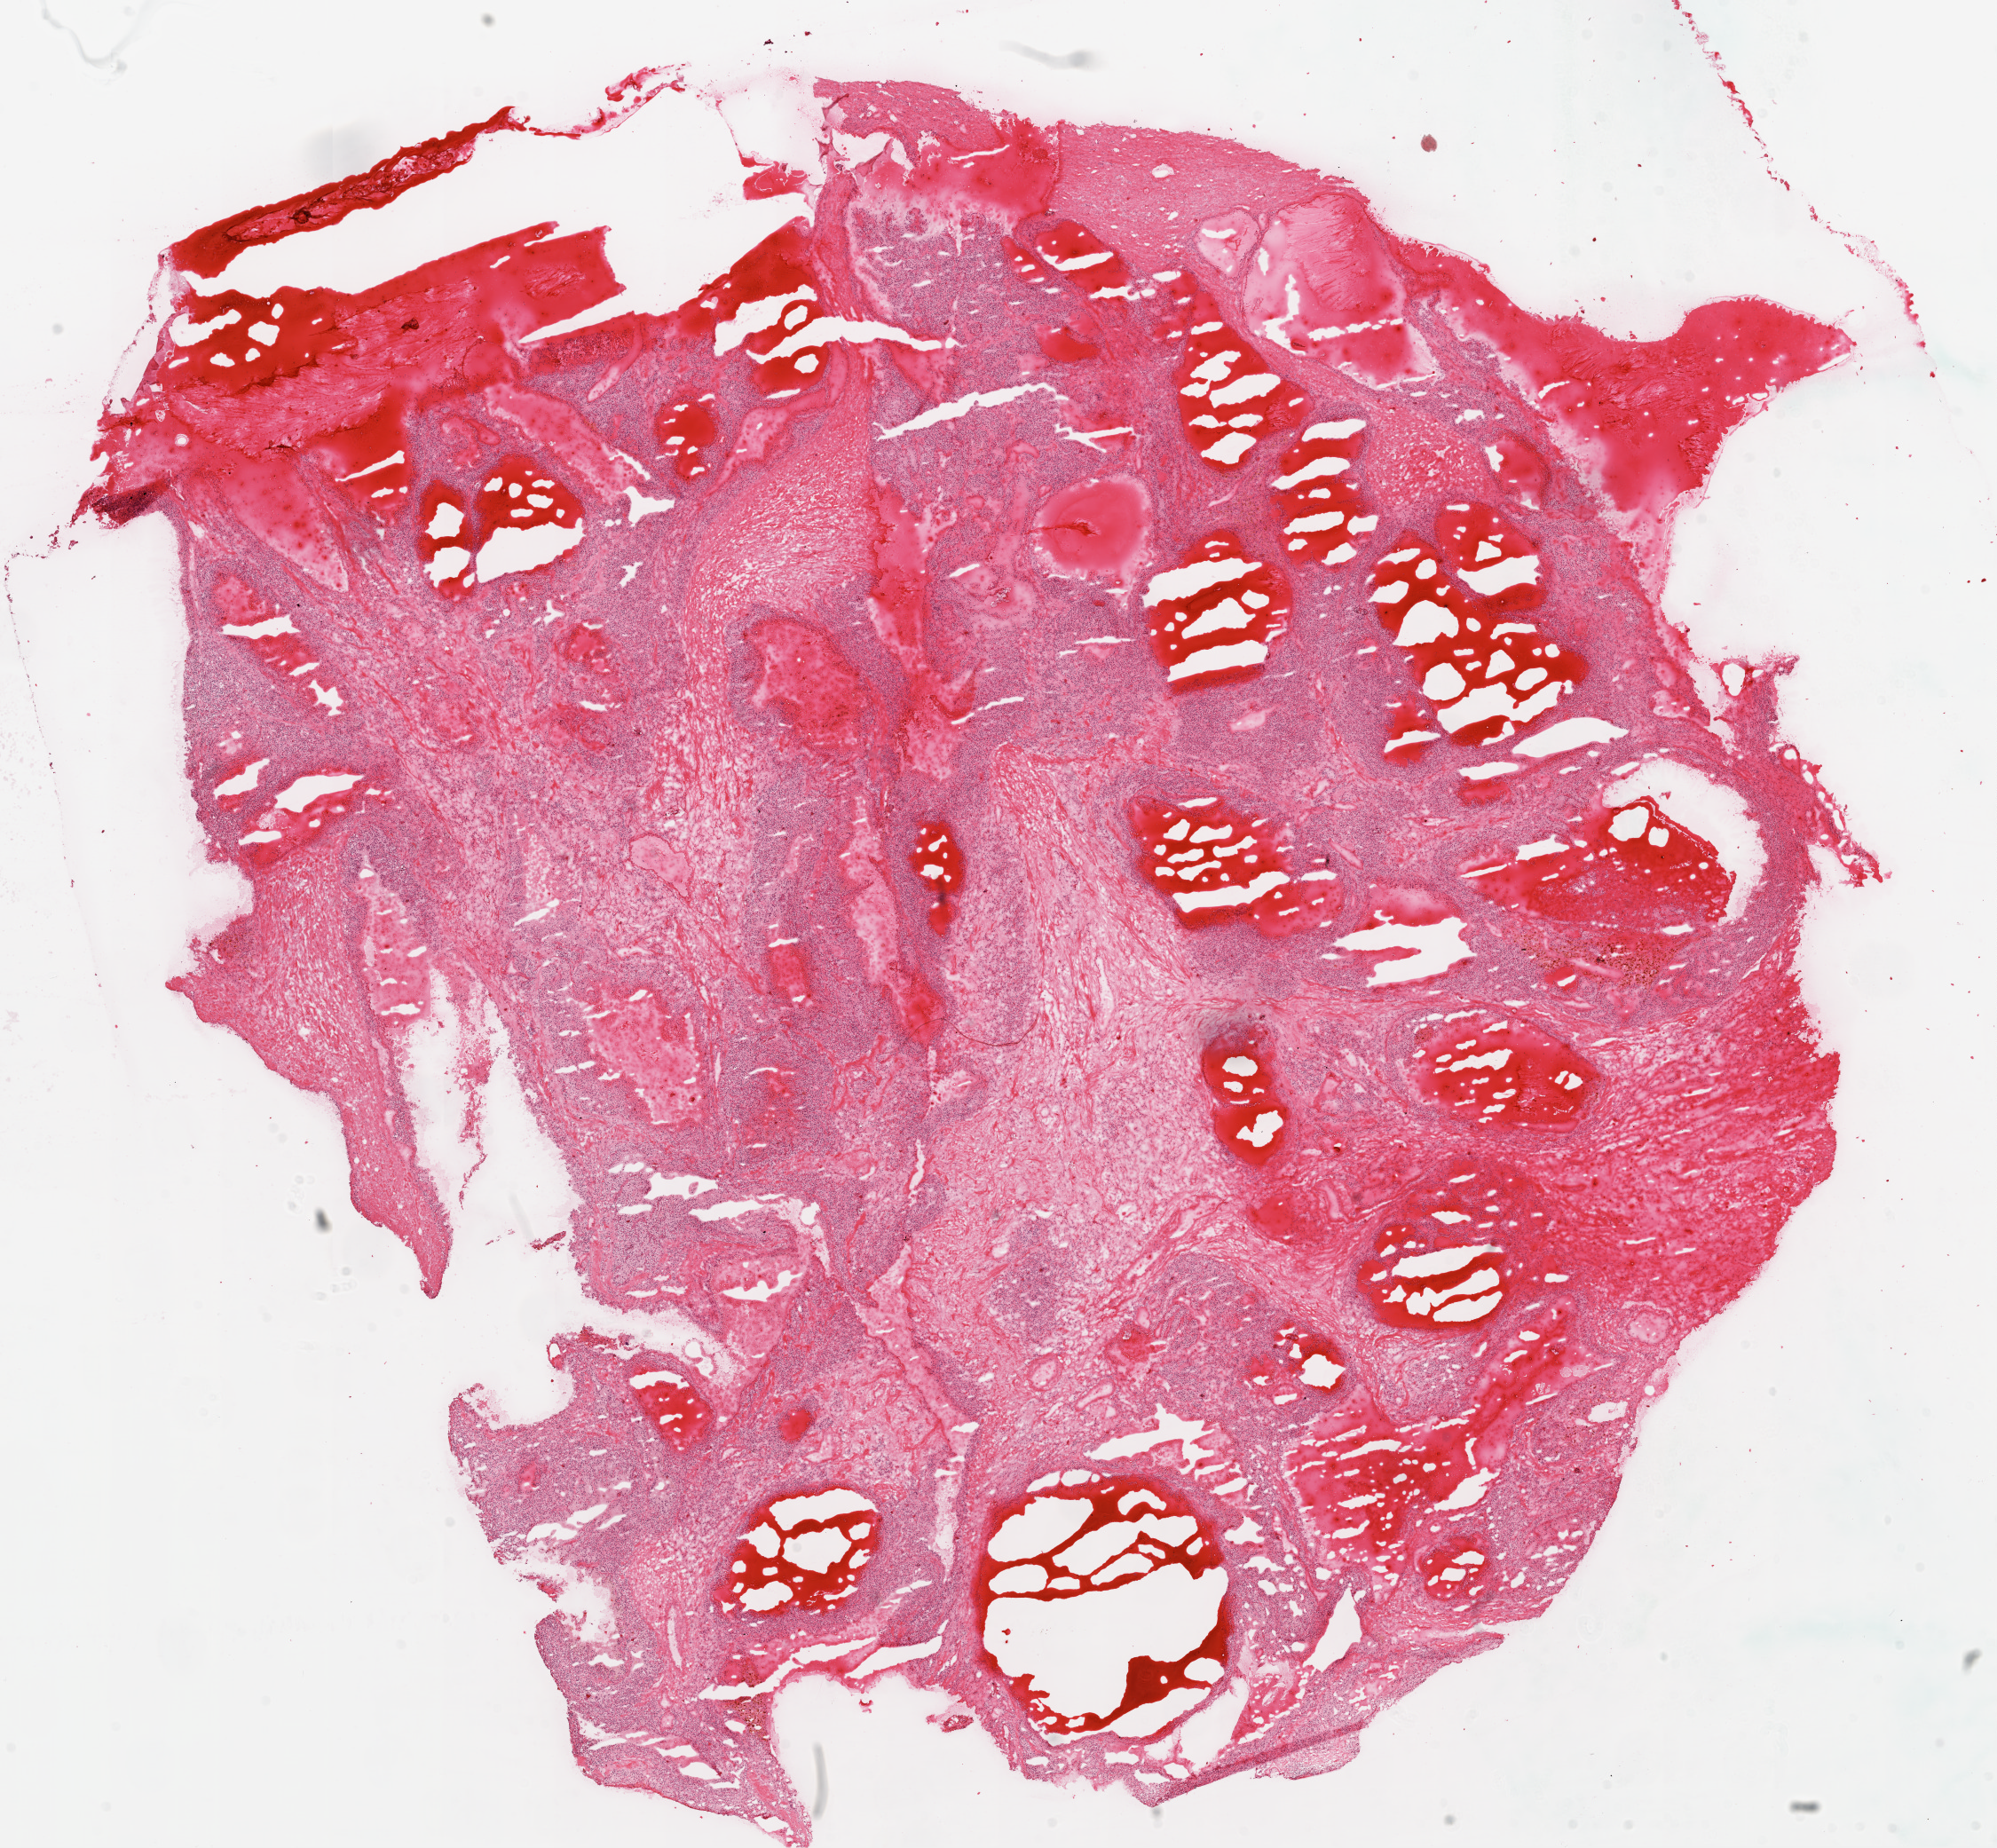
Whole-slide histology image, Hematoxylin and eosin (H&E) stained, whole scanned area (about 18.1 x 16.7 mm) shown as a low-resolution overview, frozen section, sample: primary tumour, kidney. Male patient; age at initial diagnosis 36 years. Histologic grade: G2 (moderately differentiated). Slide review estimates, as recorded: tumour cells 70%, tumour nuclei 75%, normal cells 5%, stromal cells 25%, necrosis 0%.
- diagnosis: Clear cell adenocarcinoma, NOS
- AJCC pathologic stage: III